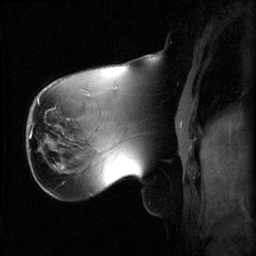
Breast MRI (dynamic contrast-enhanced), one sagittal slice; position 18 of 60 along the scan axis; 3 images stored at this slice position (order not interpretable as contrast timing); 1.5 T; TE 4.2 ms, TR 8.2 ms; 2.2 mm slice thickness; 256 × 256 image matrix, field of view 220 × 220 mm. Patient: female, 62 years.
Structures marked on this image (semi-automatically segmented with operator editing):
- analysis volume of interest (the breast-tissue region the enhancement analysis was run in; not a lesion): bounding box <26,126,59,165> (left, top, right, bottom; pixels)
- tumour enhancement mask (voxels above the 70 % enhancement threshold inside the analysis volume of interest): <30,132,31,139>